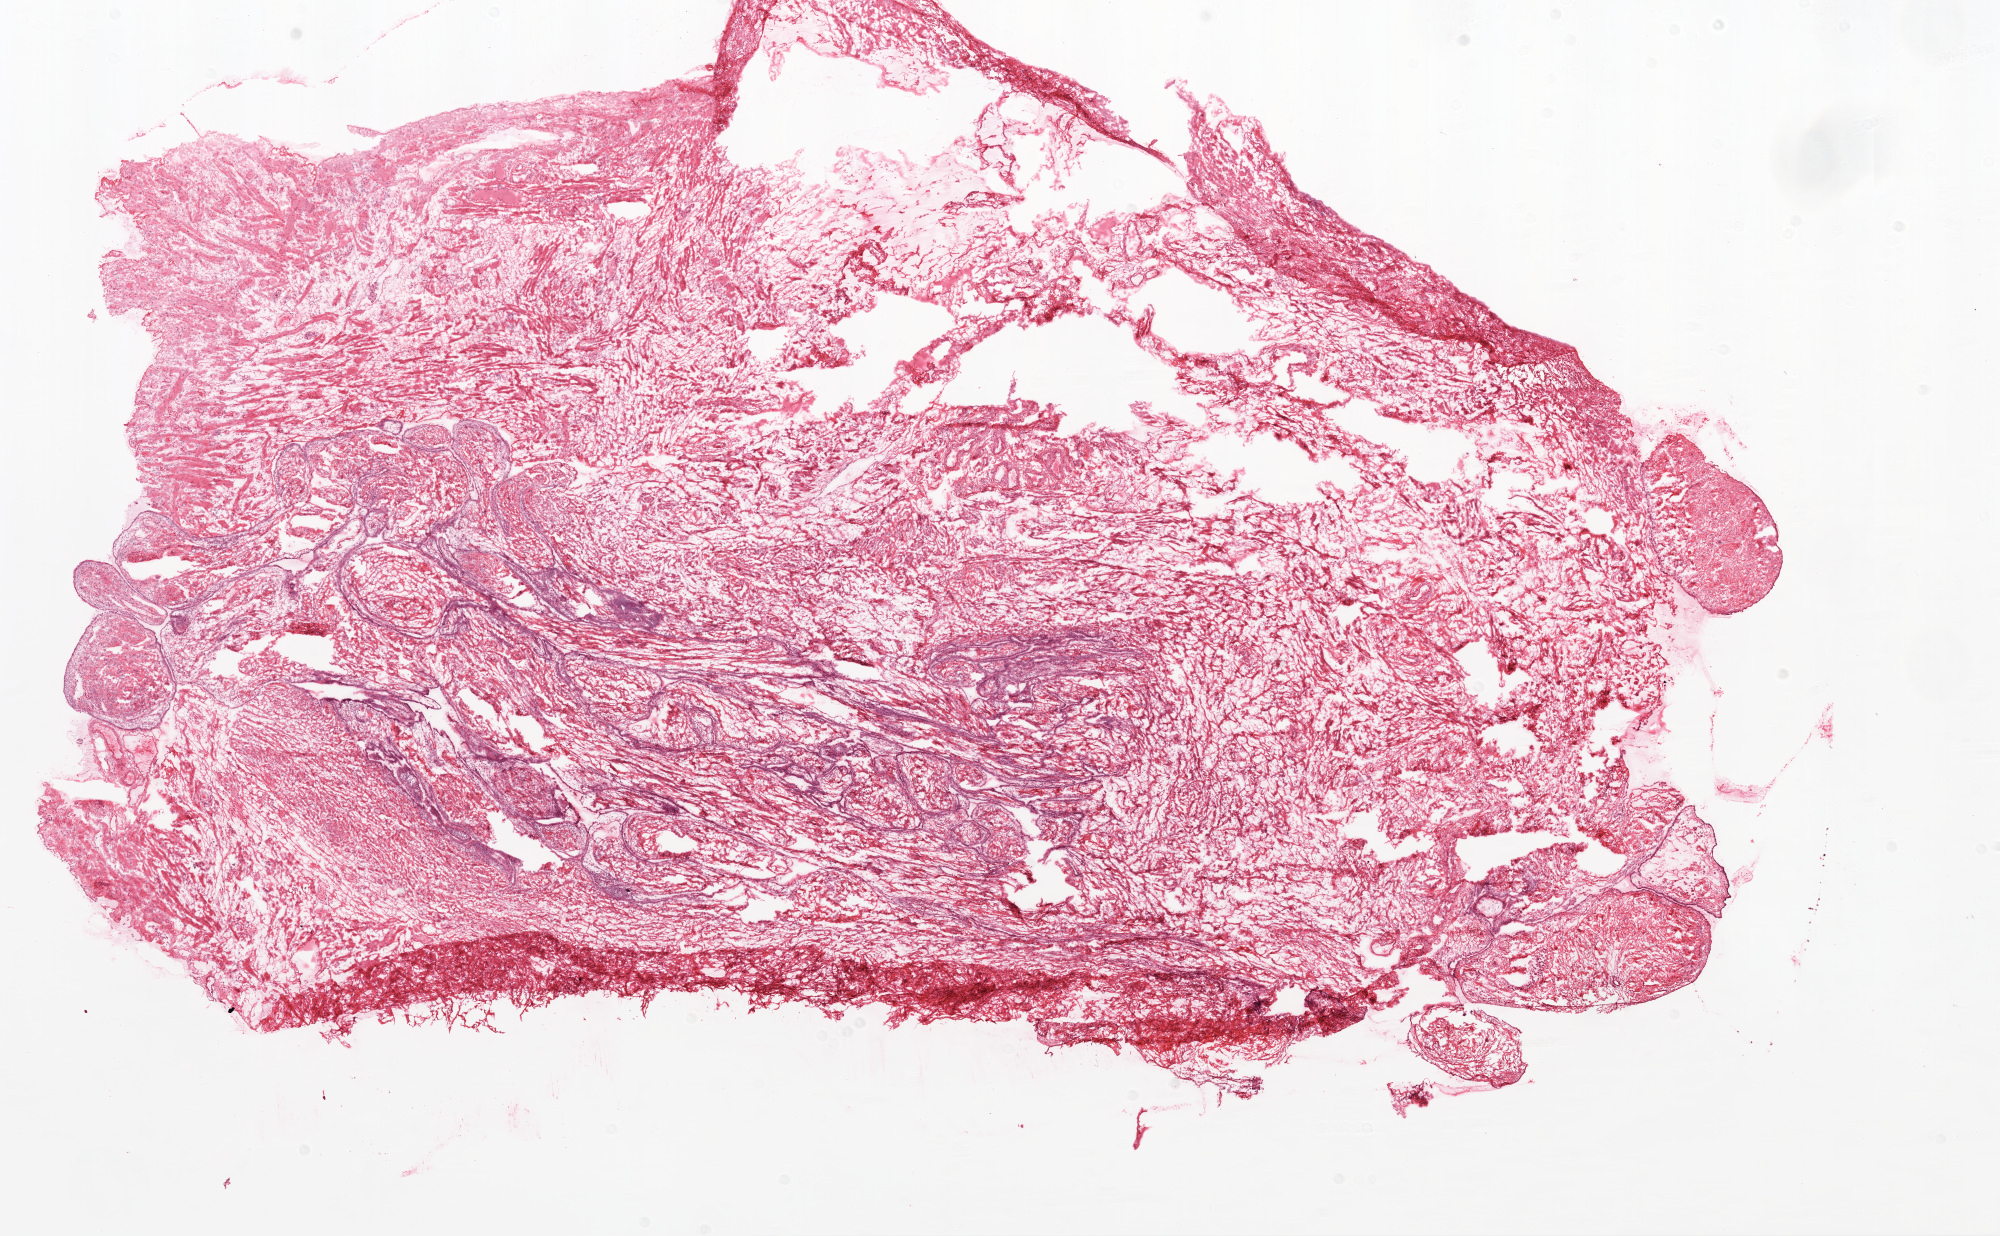
Digitized H&E-stained tissue section (whole slide) — whole scanned area (about 16.0 x 9.9 mm, slide scanned at 20x) shown as a low-resolution overview. Frozen section from the top of the tissue portion. Solid tissue normal (non-tumour tissue) sample from the ovary. Female patient; age at initial diagnosis 65 years.
This section: solid tissue normal (non-tumour) sample from the same patient. Patient diagnosis: Serous cystadenocarcinoma, NOS.